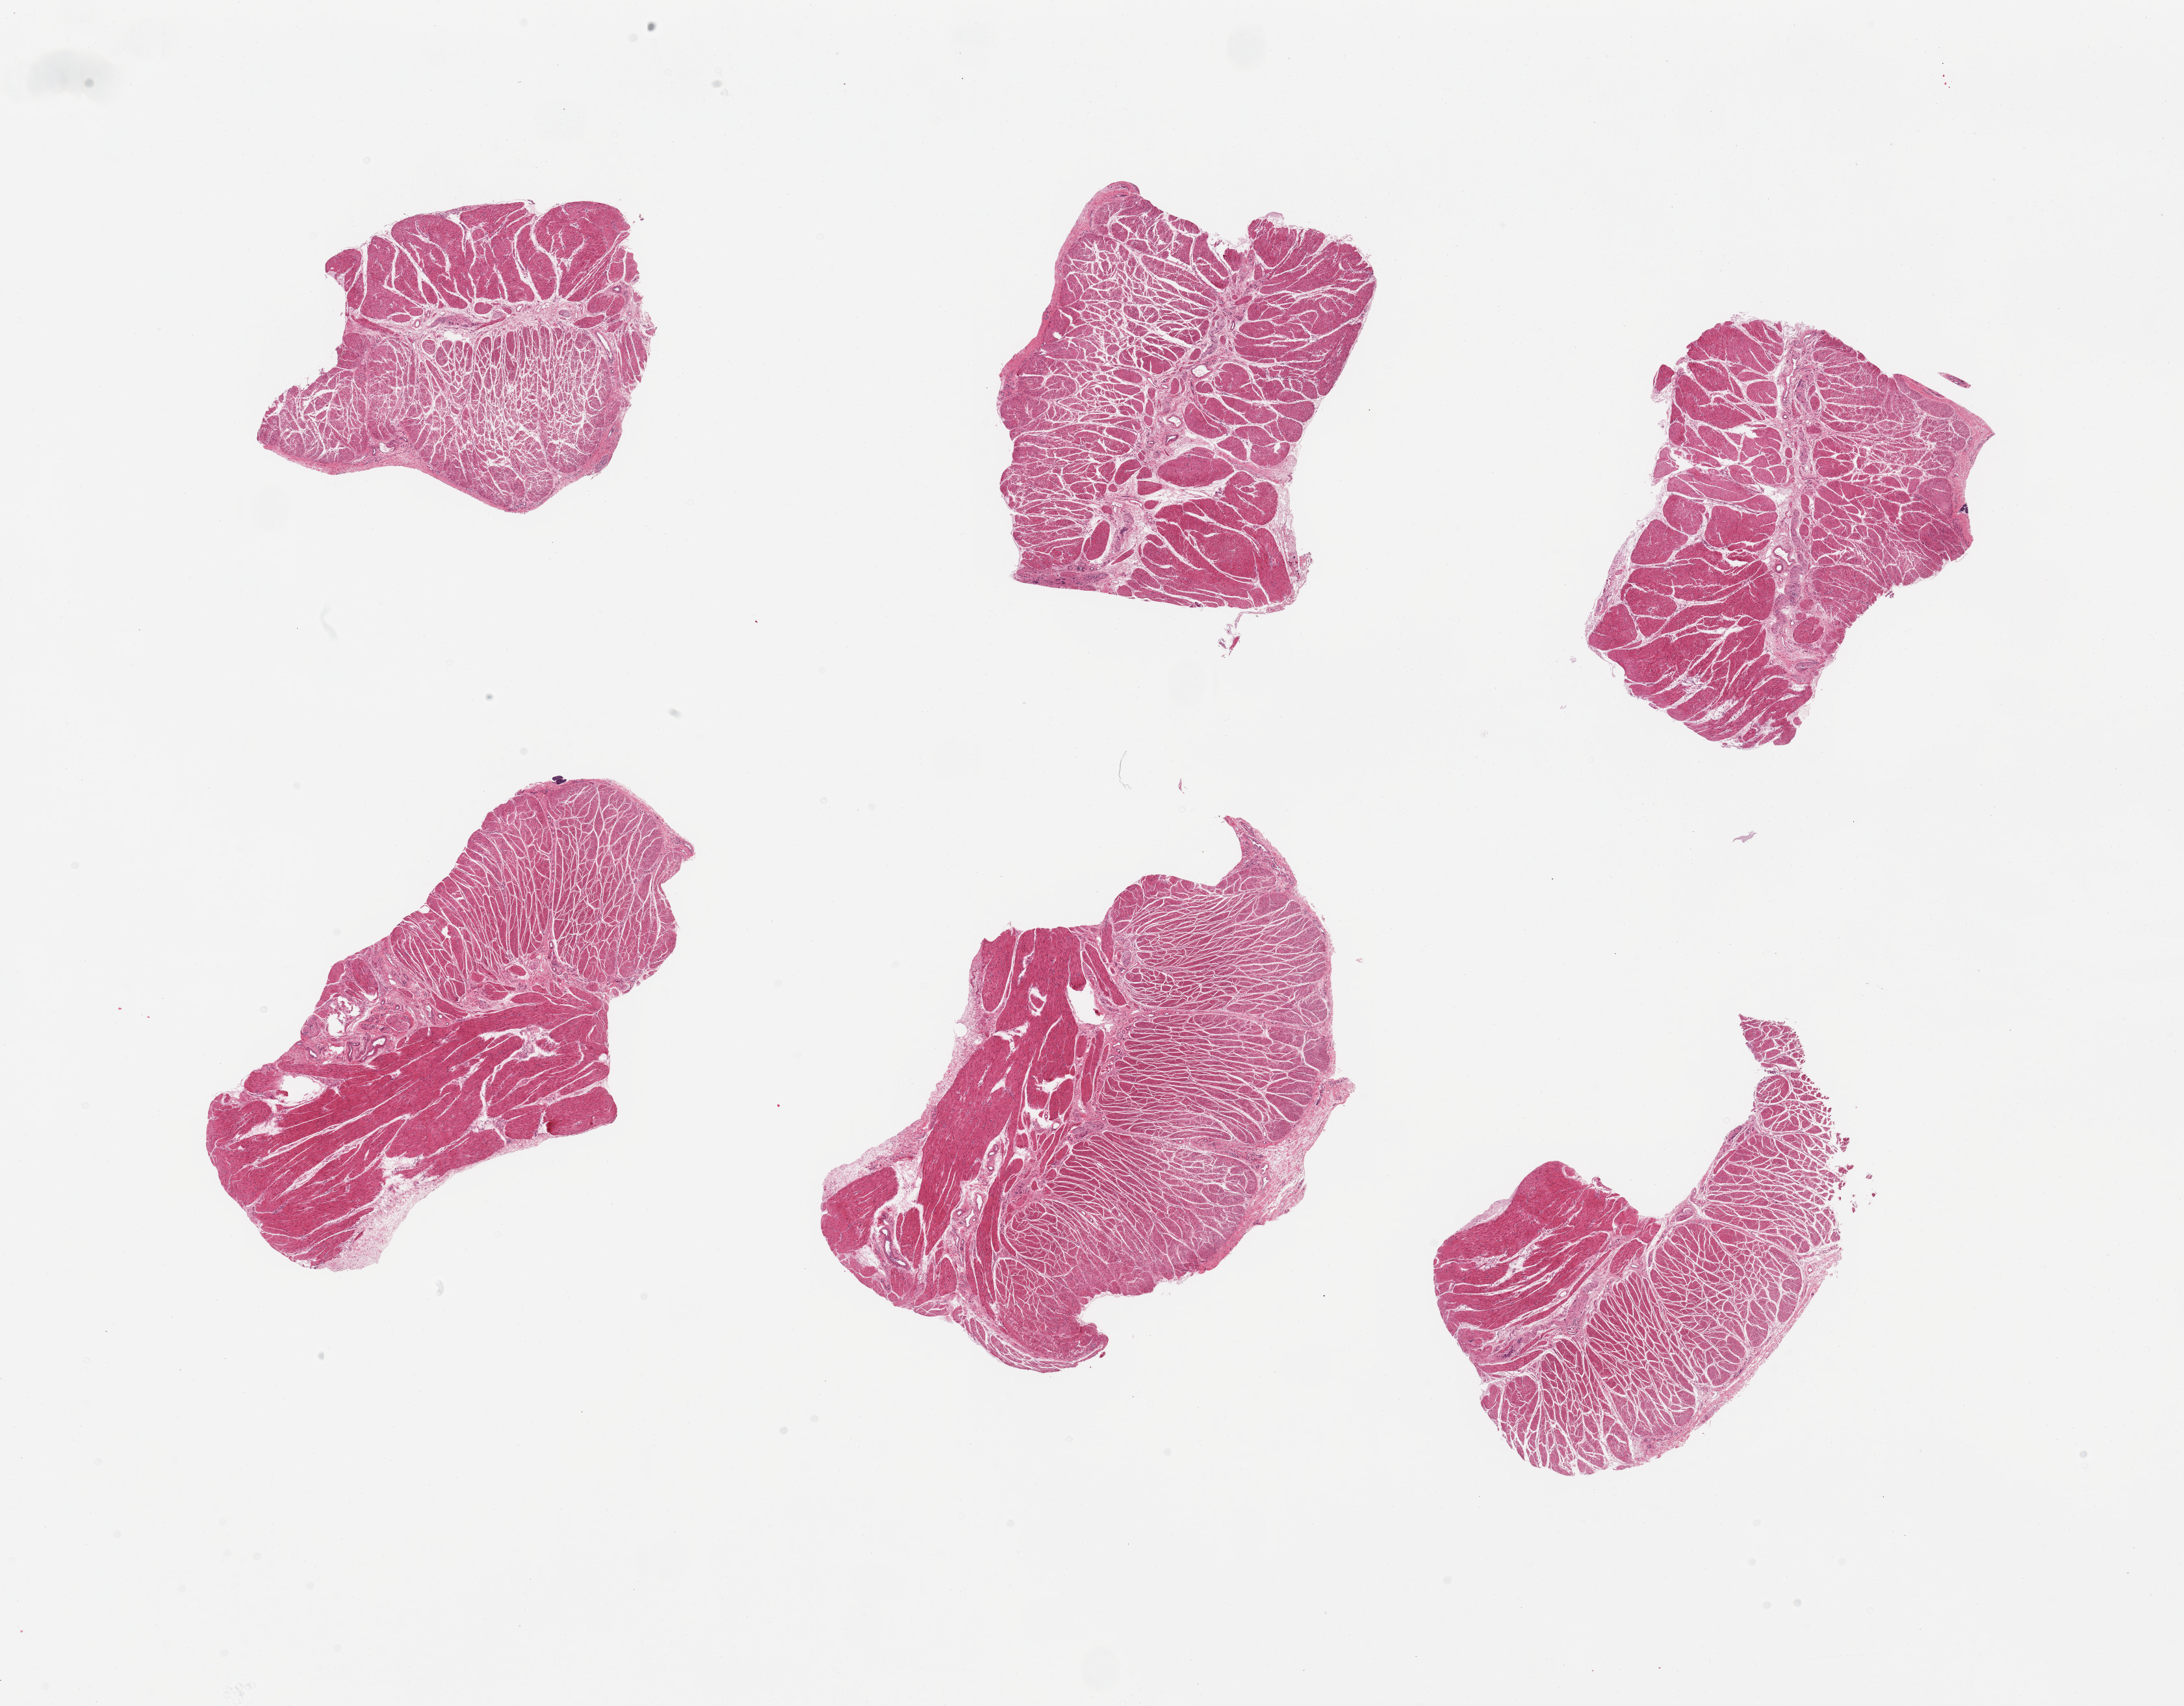
Whole-slide image, H&E stain, brightfield — whole scanned area (about 26.6 x 20.8 mm) shown as a low-resolution overview; PAXgene-fixed paraffin-embedded (PFPE) section; section of gastroesophageal junction (target tissue); donor tissue sample.
- pathologist's review note for this sample: 6 pieces, confirmed target muscularis